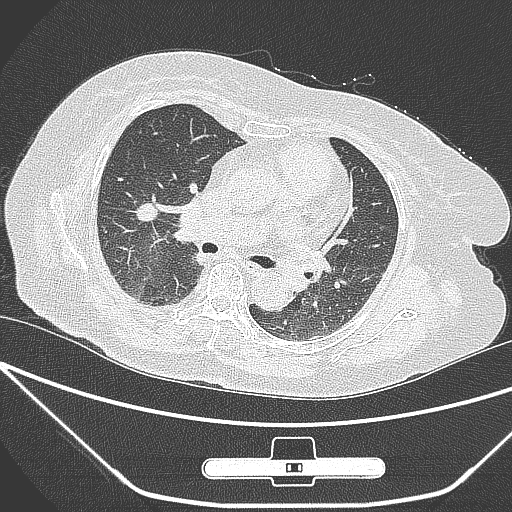
Chest CT, one axial slice; slice 156 of 245 in the series (ordered by position); 120 kVp; lung window (W 1500 / L -600 HU); 1 mm slice thickness; 512 × 512 image matrix, field of view 365 × 365 mm. Female patient, age 65 years. Case-level facts recorded for this patient, not image findings: clinical TNM (as recorded): T1c N0 M0.
Structures marked on this image (rectangle marked by the reading radiologist):
- lung tumour (recorded histology: adenocarcinoma): bounding box [x1, y1, x2, y2] px = [133, 195, 166, 224]